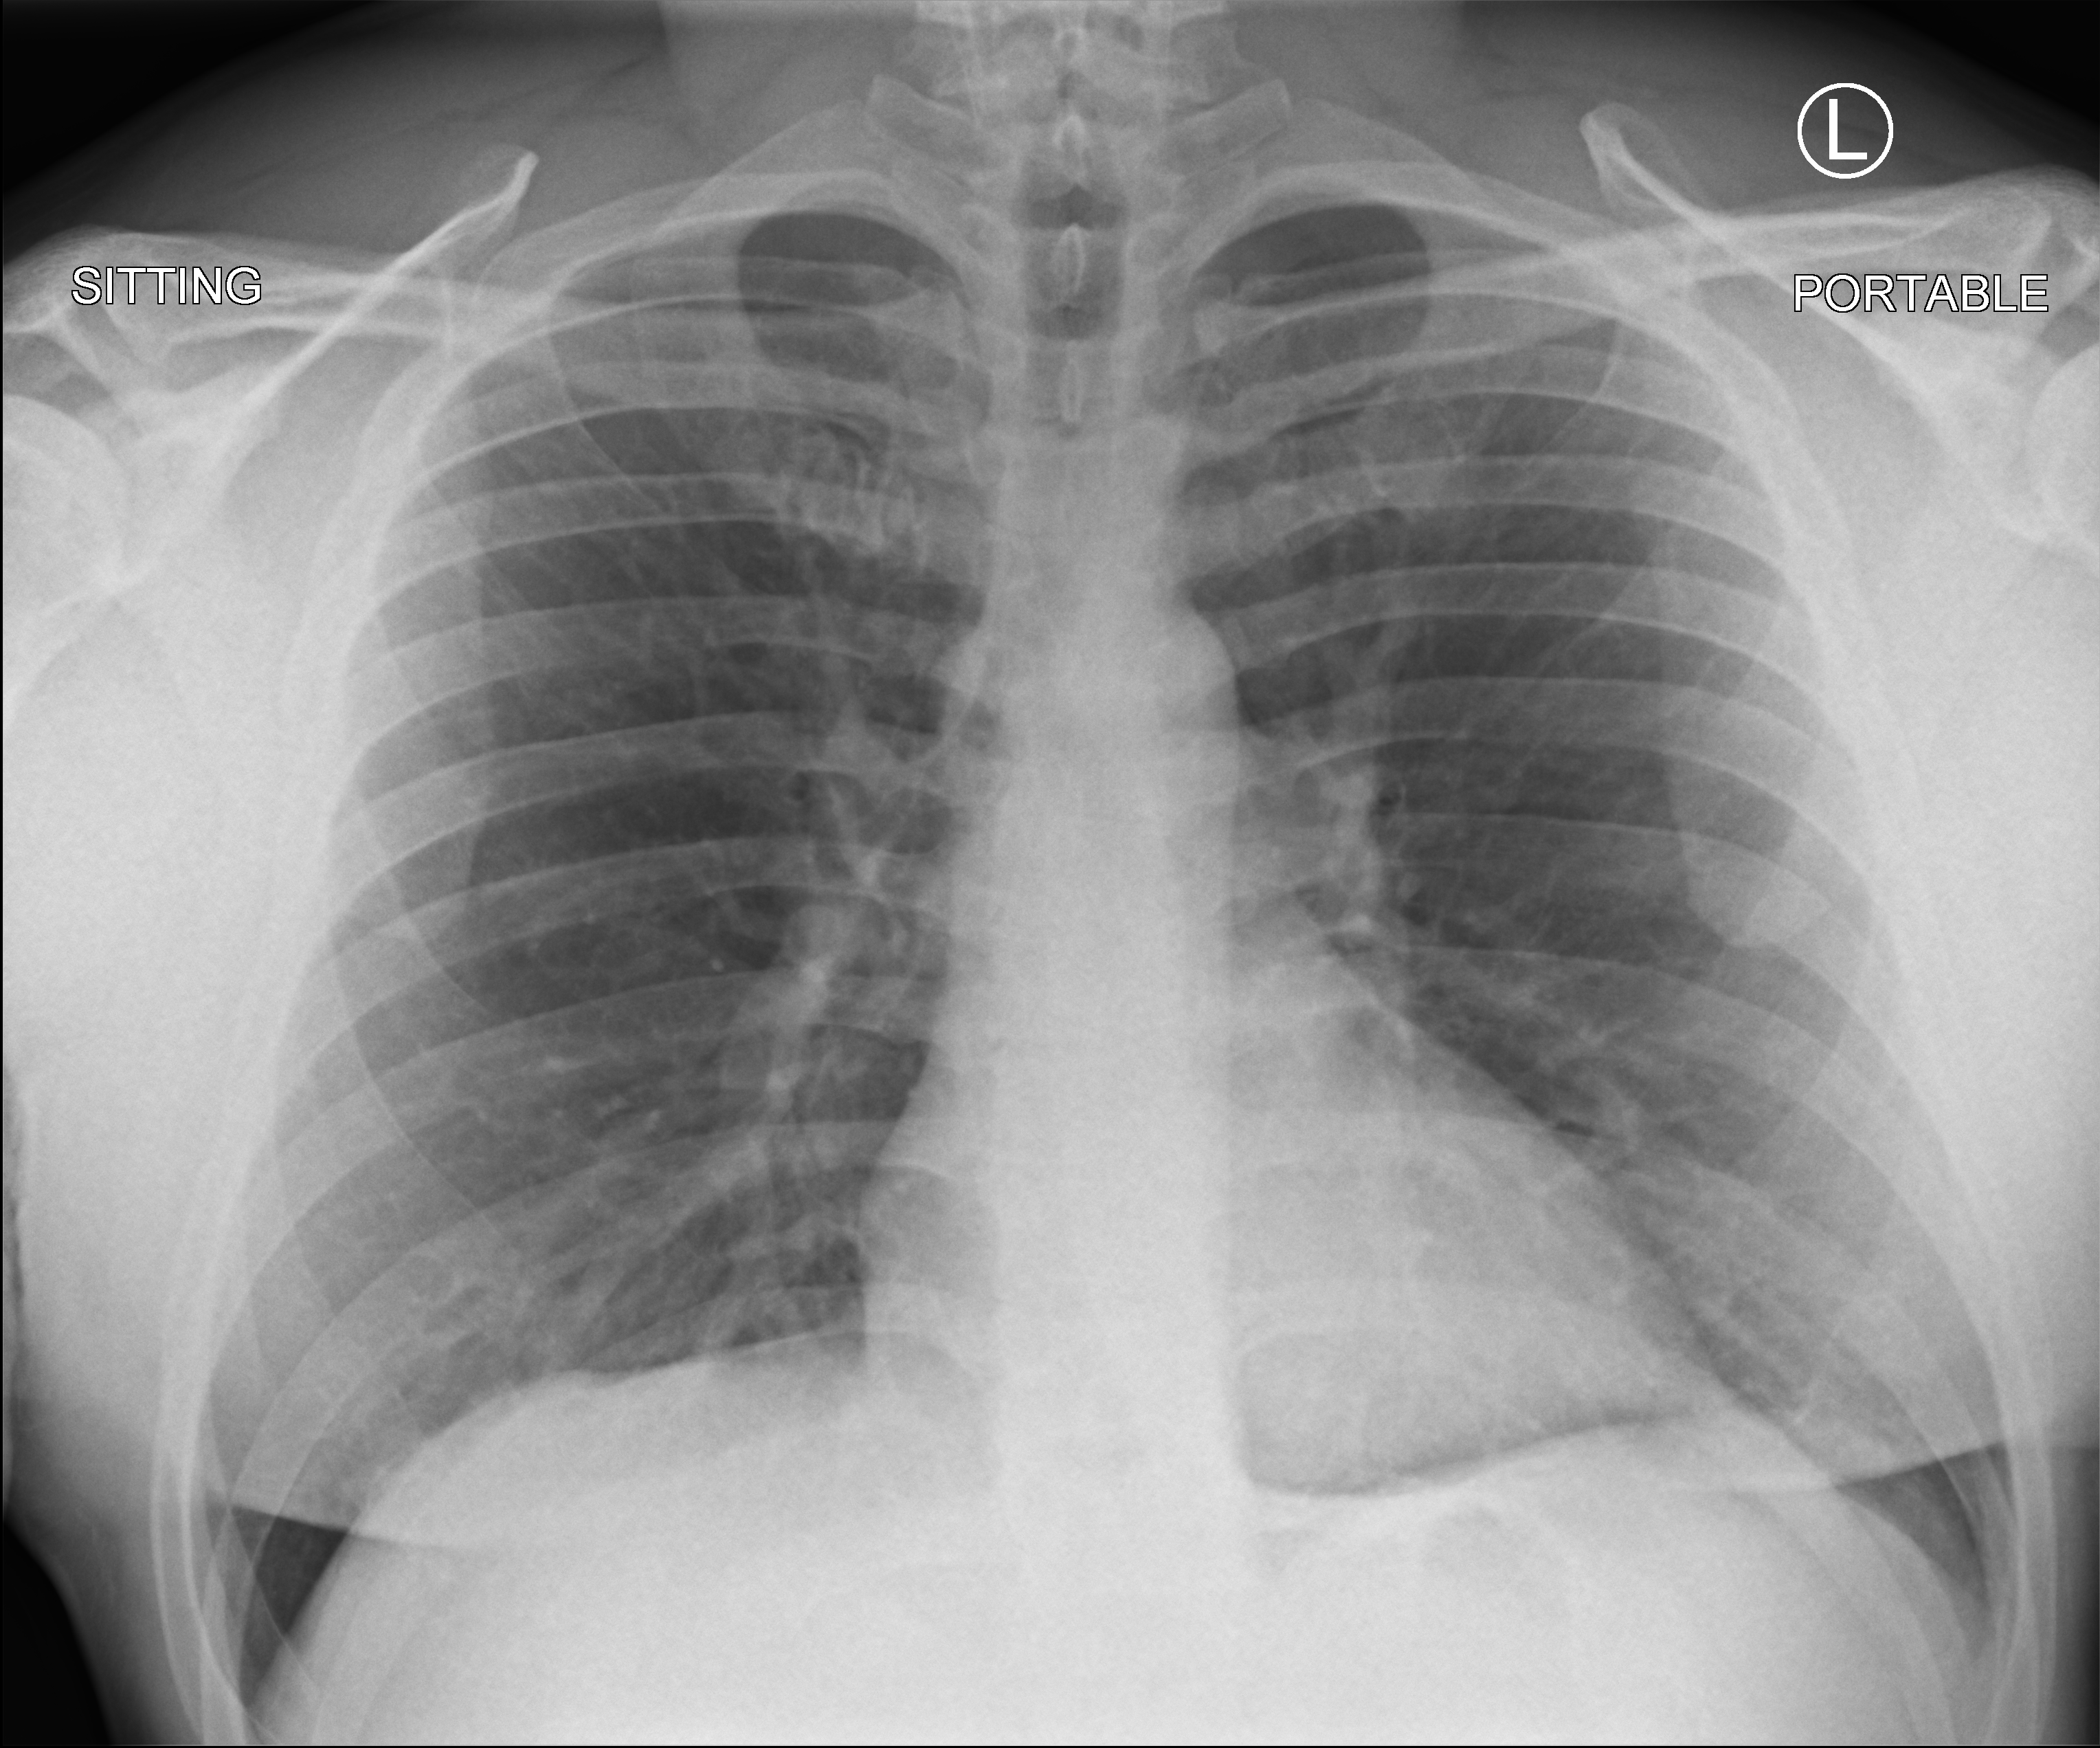
Bedside chest radiograph (computed radiography). Male patient hospitalised with COVID-19, age 18–59 years.
Hospital-stay facts (about this admission, not read from this image; timing relative to this image not recorded): mechanically ventilated during this hospital stay: no.